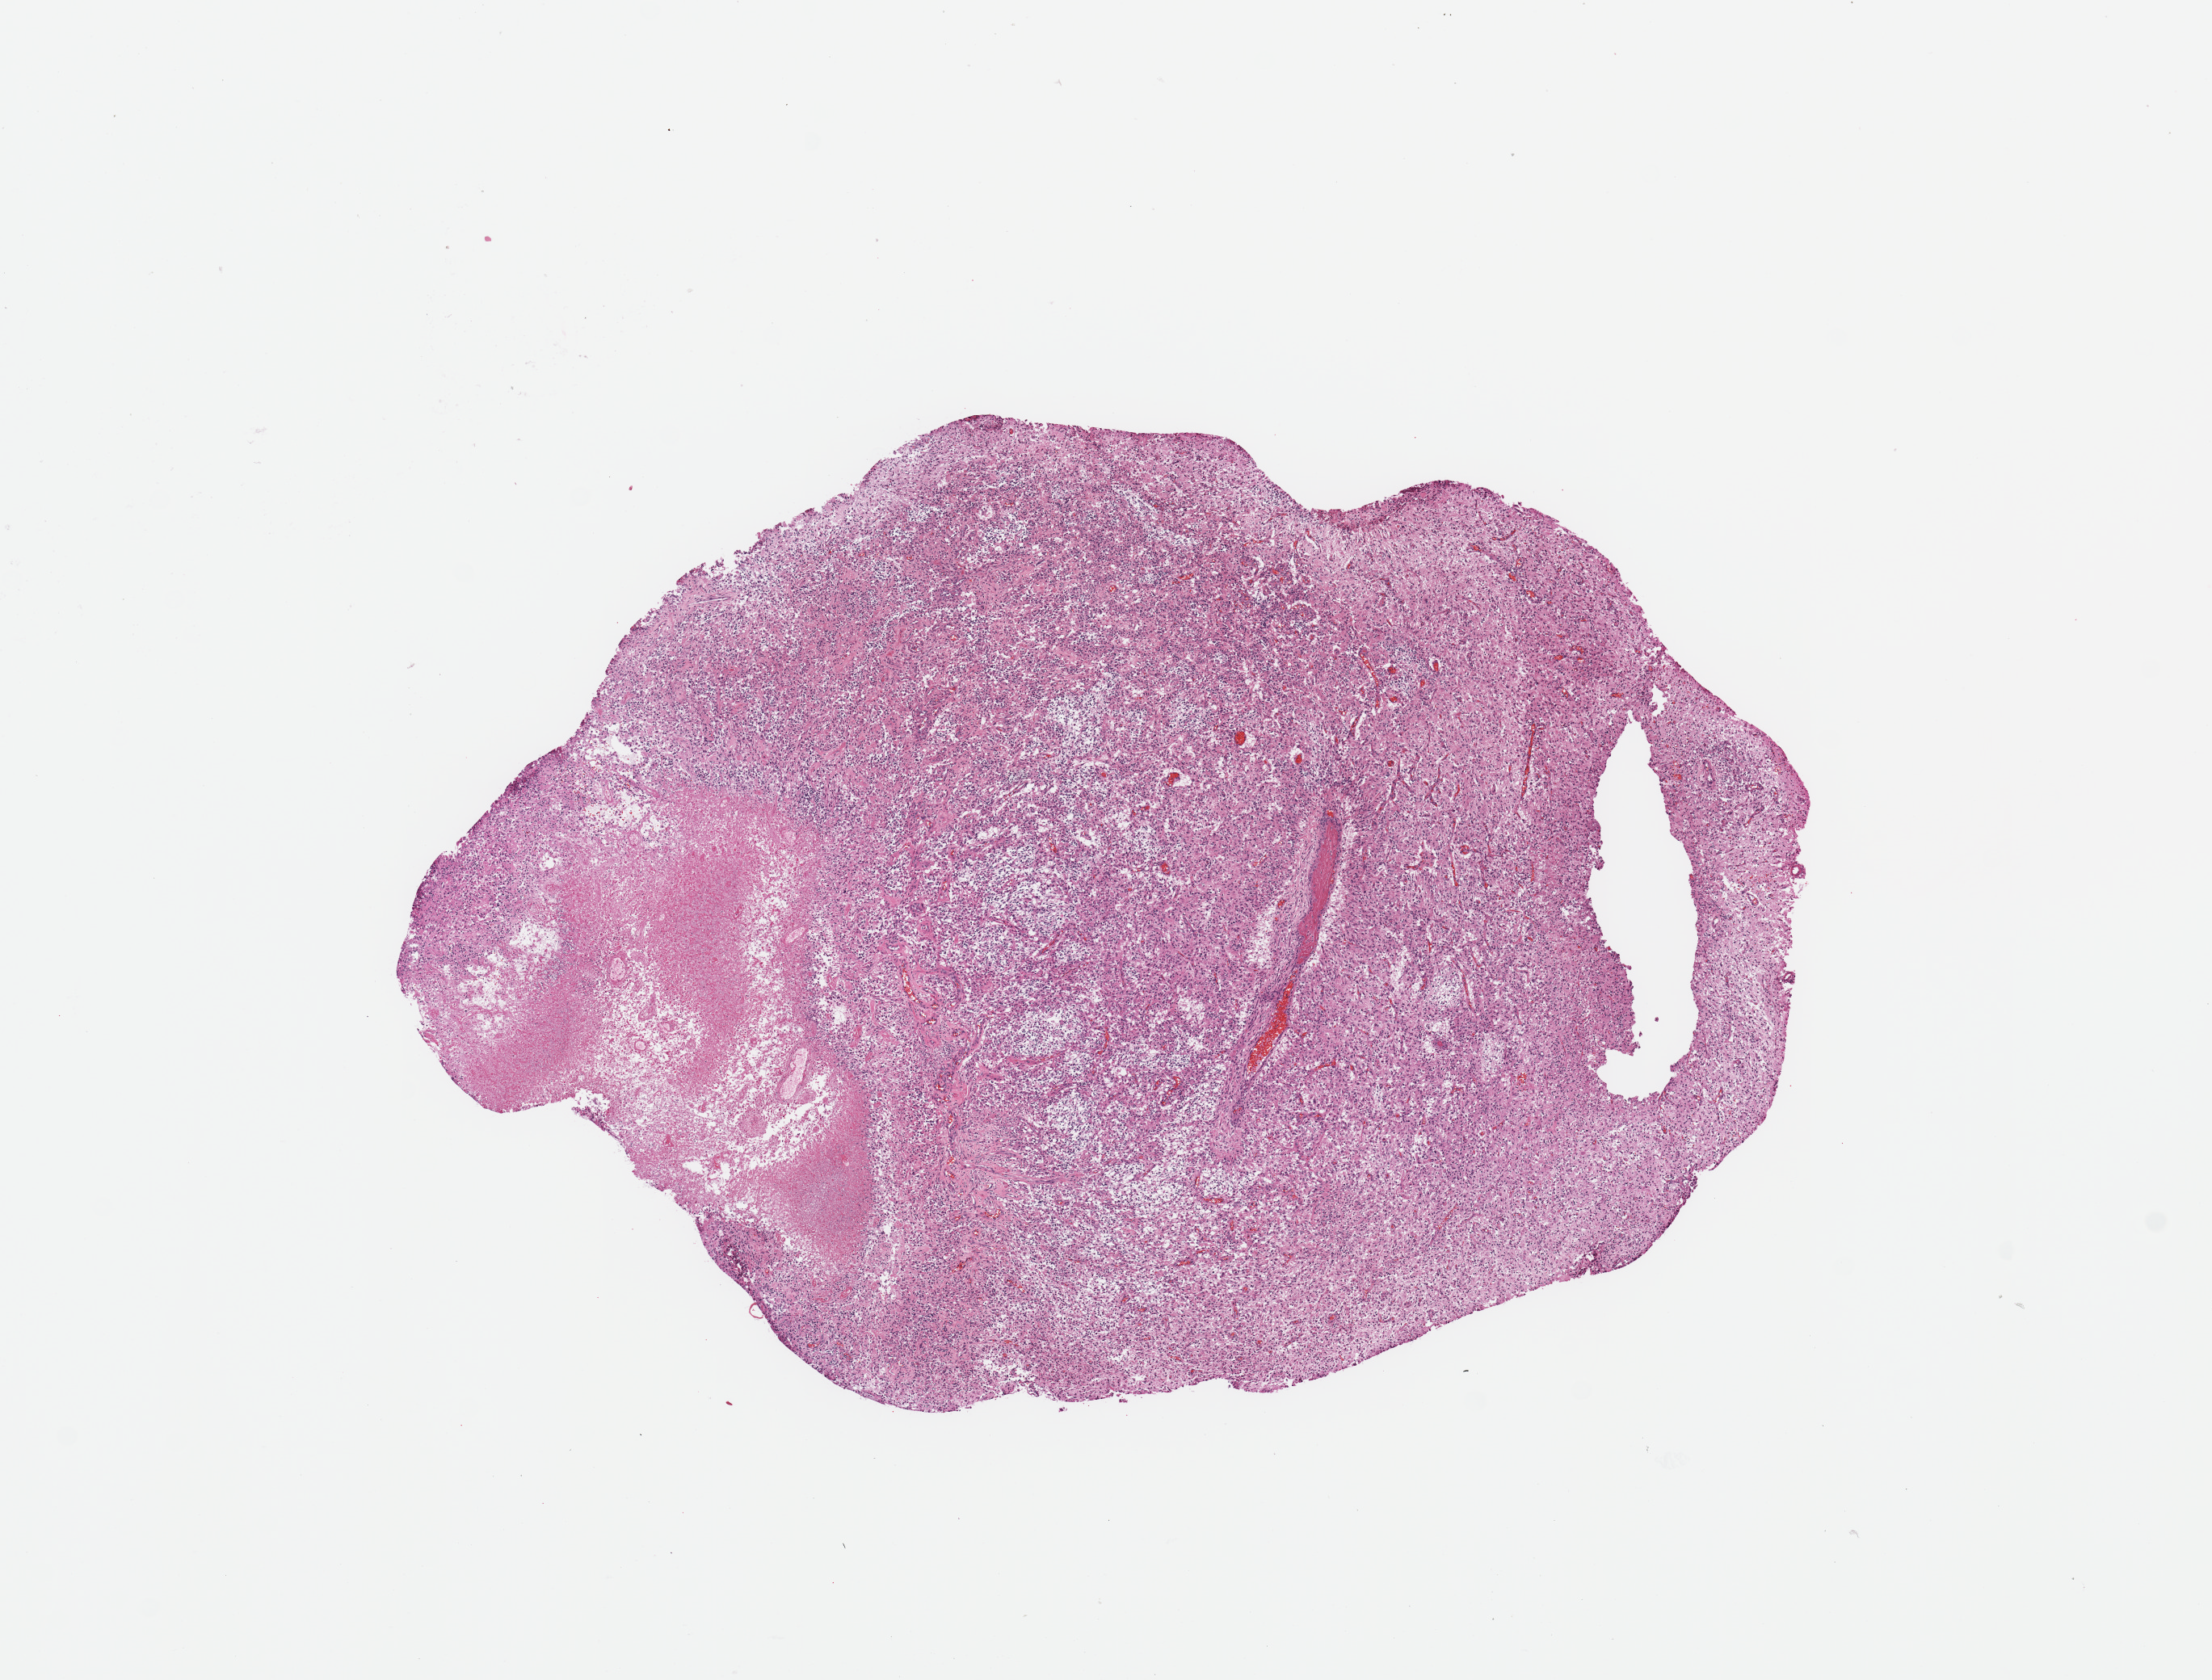
Digitized H&E tissue section (whole slide), a low-resolution overview of the entire scanned area, about 10.8 x 8.2 mm (slide scanned at 20x), tumour tissue sample, sampled site: temporal cortex. Patient: male, age 50 years.
Diagnosis: Glioblastoma.